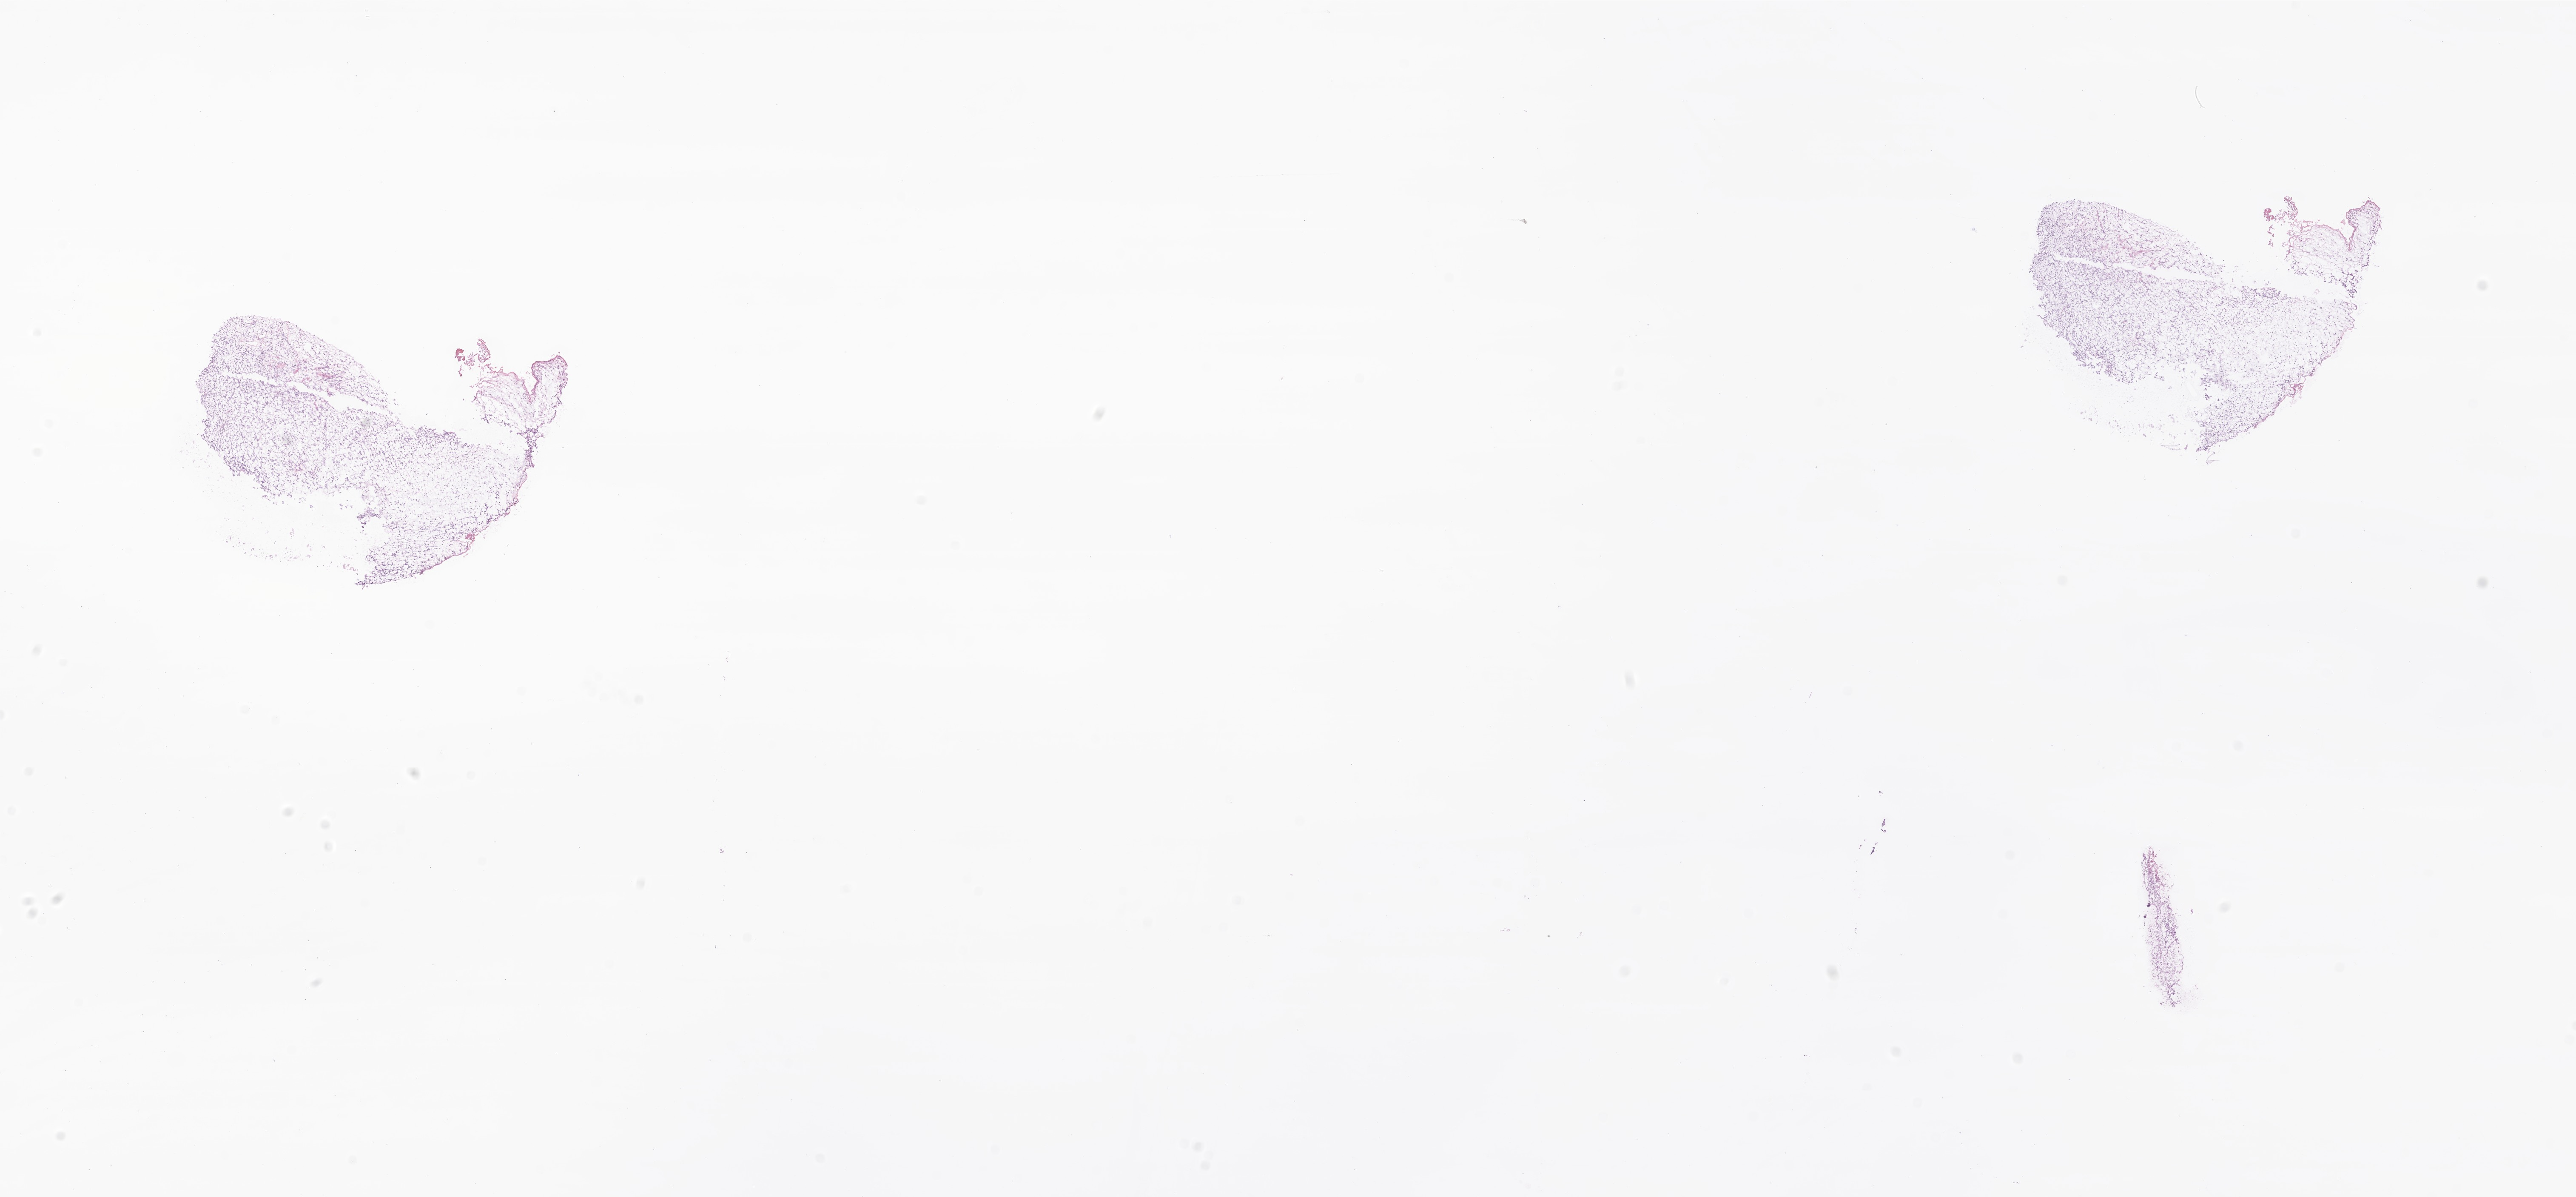
H&E whole-slide image of tumor tissue from the abdomen, a low-resolution overview of the entire scanned area, about 25.5 x 11.9 mm. Frozen section. Patient female; age 525 days.
Diagnosis (ICD-O-3 morphology term): Embryonal rhabdomyosarcoma, NOS.